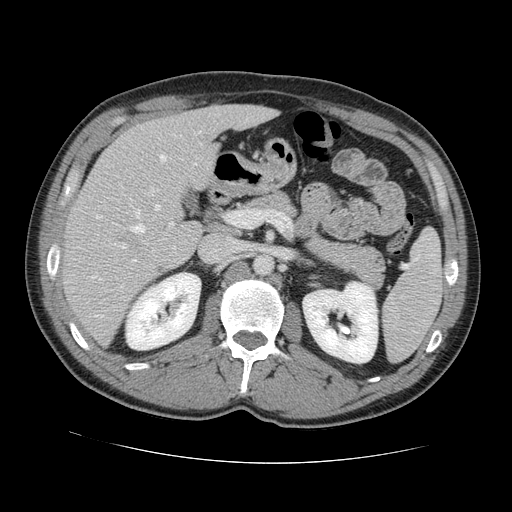
Contrast-enhanced abdominal CT, one axial slice. Slice 74 of 131 in the series (ordered by position). 120 kVp. Intravenous contrast given. Soft-tissue window (W 400 / L 40 HU). 2.5 mm slice thickness. 512 × 512 image matrix. Male patient, age 40 years. Case-level facts recorded for this patient, not image findings: diagnosis: colorectal cancer liver metastases, imaged before liver resection; multiple liver metastases: yes; largest metastasis: 2.9 cm; chemotherapy before resection: yes.
Outlined on this slice (expert manual segmentation):
- hepatic veins: box from (x=92, y=153) to (x=167, y=317) px
- liver: (x=65, y=106)–(x=273, y=343)
- planned liver remnant (the part of the liver to remain after resection): (x=107, y=106)–(x=273, y=195)
- portal vein (with intrahepatic branches): (x=132, y=187)–(x=234, y=263)
- liver metastasis: (x=125, y=234)–(x=140, y=247)